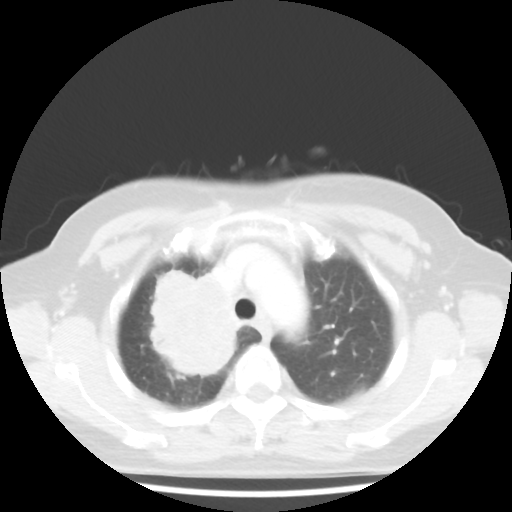
Chest CT, one axial slice. Slice 35 of 44 in the series (ordered by position). Reconstruction kernel STANDARD. 100 kVp. Lung window (W 1500 / L -600 HU). 5 mm slice thickness. 512 × 512 image matrix, field of view 316 × 316 mm. Patient: female, 62 years. Case-level facts recorded for this patient, not image findings: clinical TNM (as recorded): T3 N0 M0; histopathological grade: G3.
Annotated regions visible in this slice (rectangle marked by the reading radiologist):
- lung tumour (recorded histology: small cell carcinoma): bounding box (x1, y1, x2, y2) in pixels: (137, 256, 245, 387)